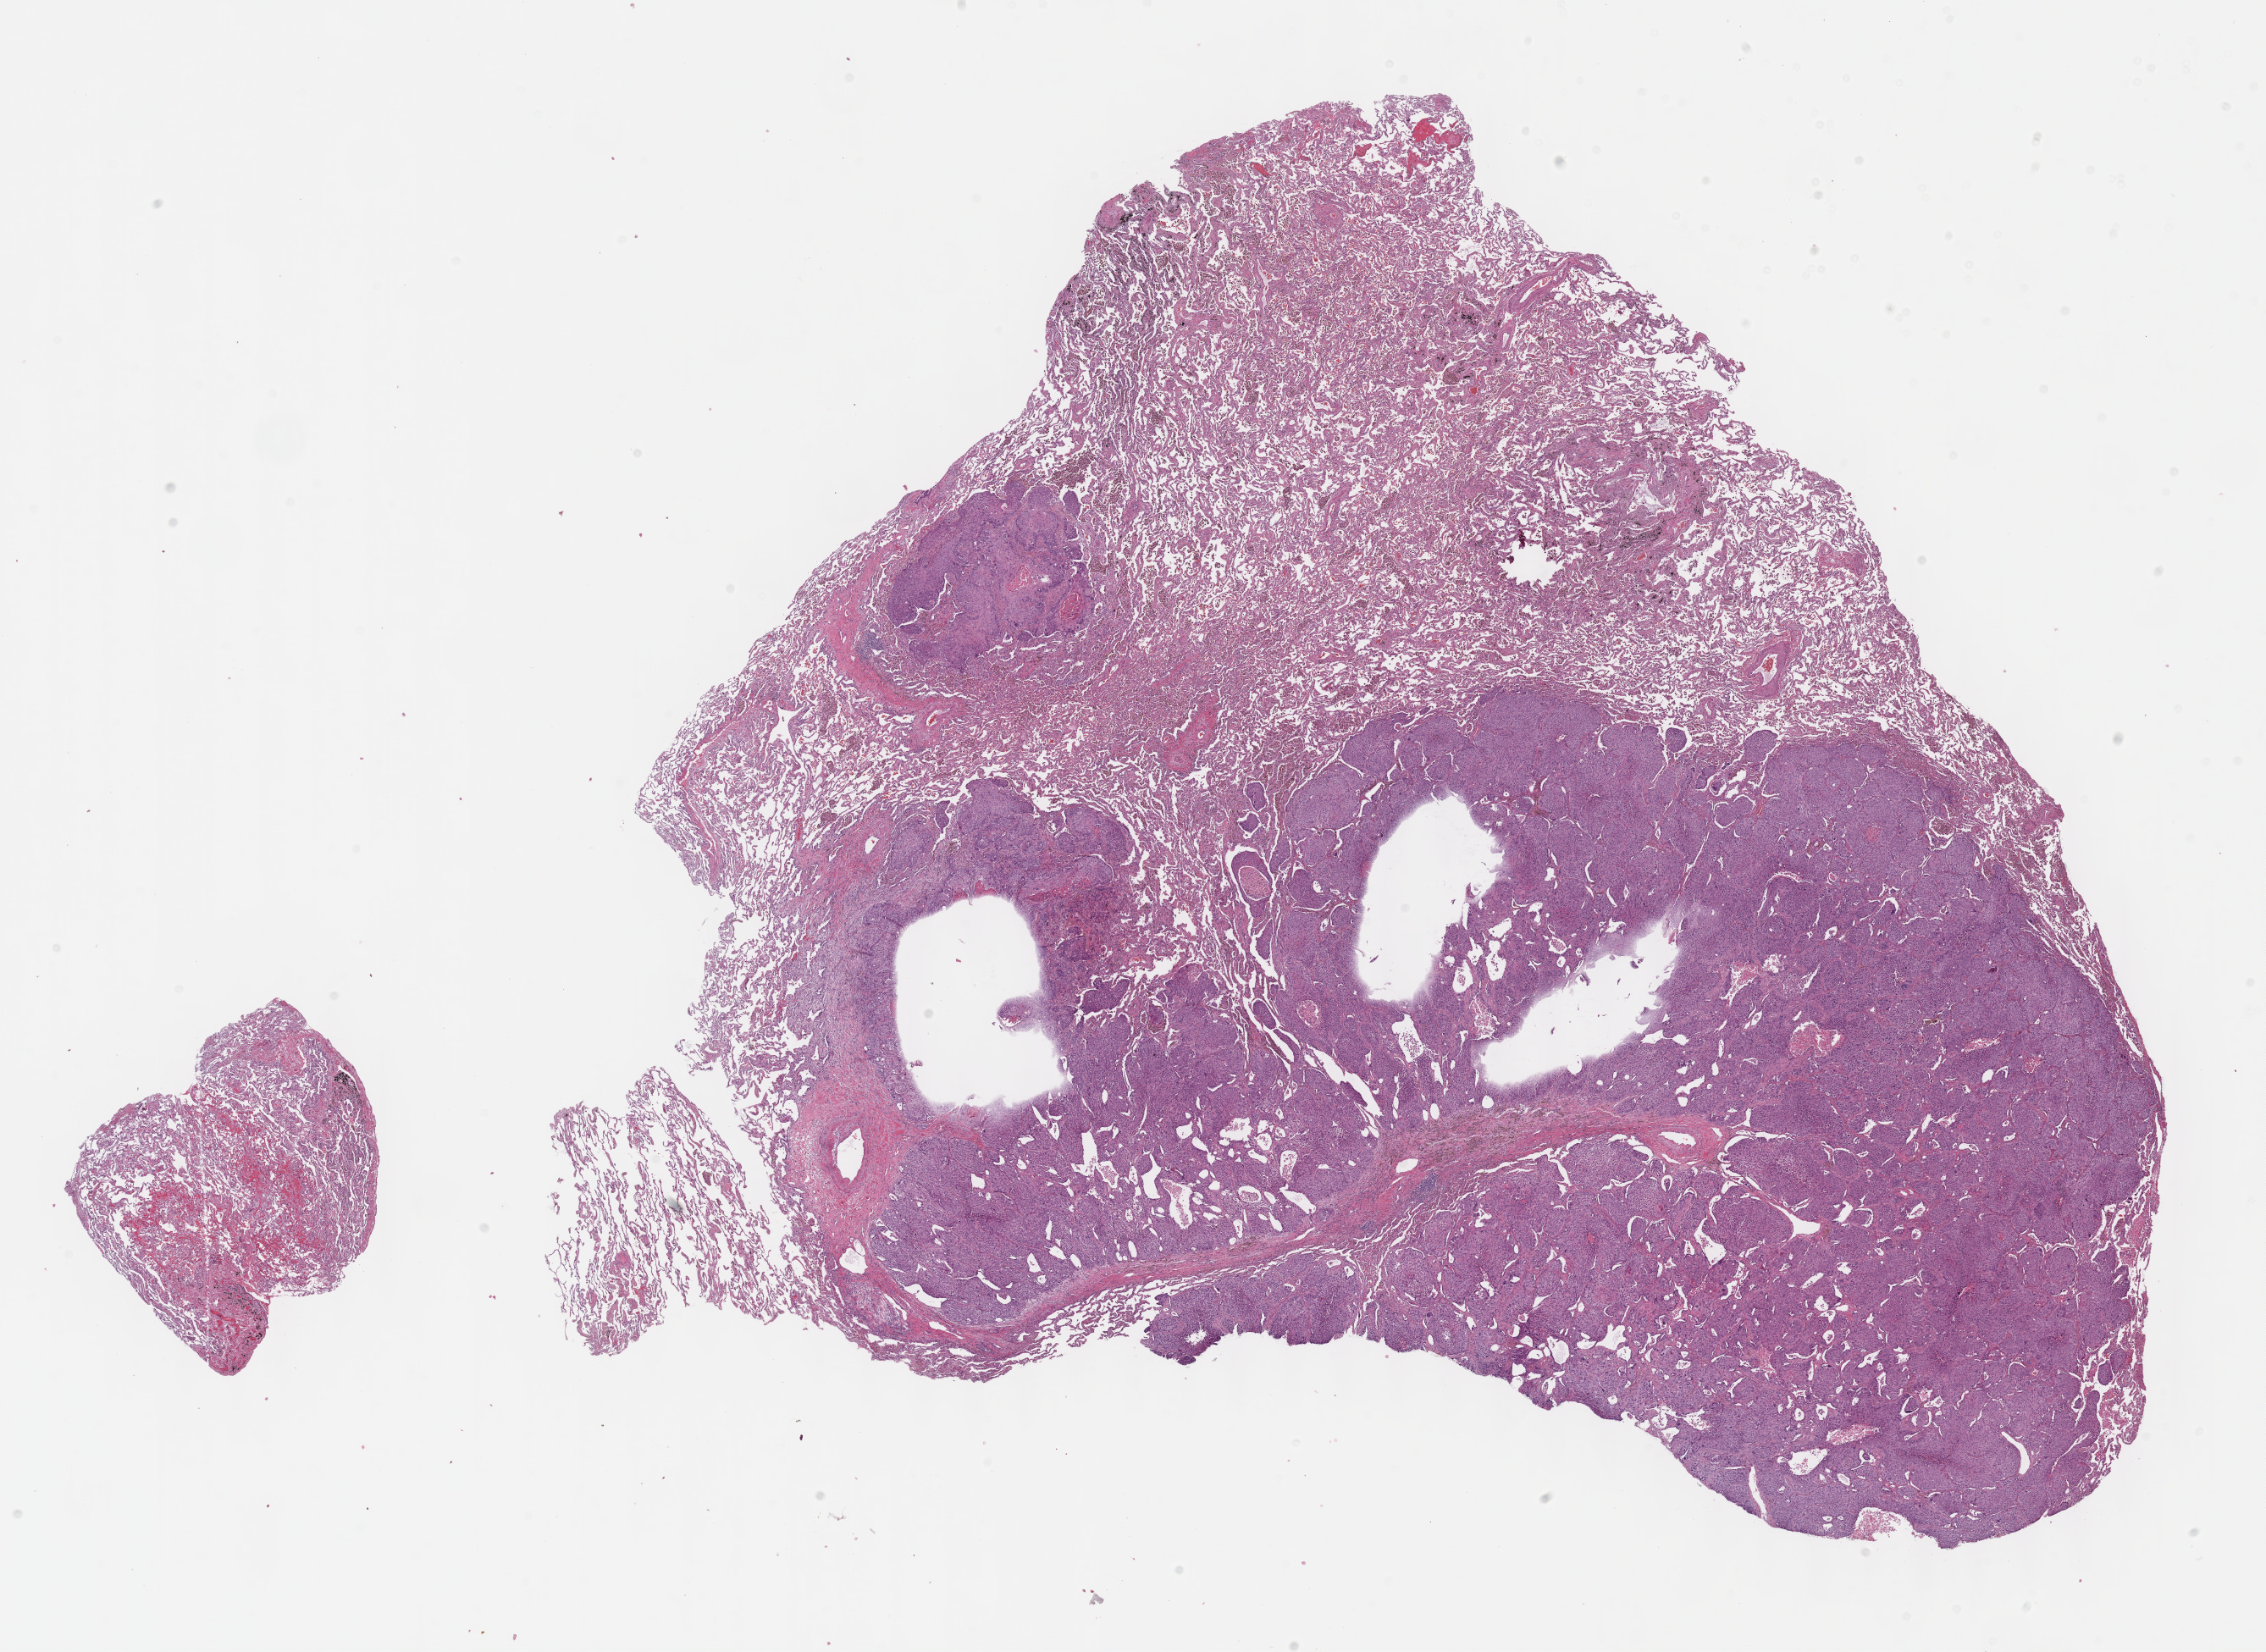
H&E-stained whole-slide image — shown as a low-resolution overview of the whole scanned area (about 21.6 x 15.8 mm, acquisition: 40x scan). Formalin-fixed paraffin-embedded (FFPE) diagnostic section. Sample: primary tumour, lung. Female, age 58 years at initial diagnosis.
* AJCC pathologic stage: IA
* pathologic diagnosis: Squamous cell carcinoma, NOS (upper lobe, lung)